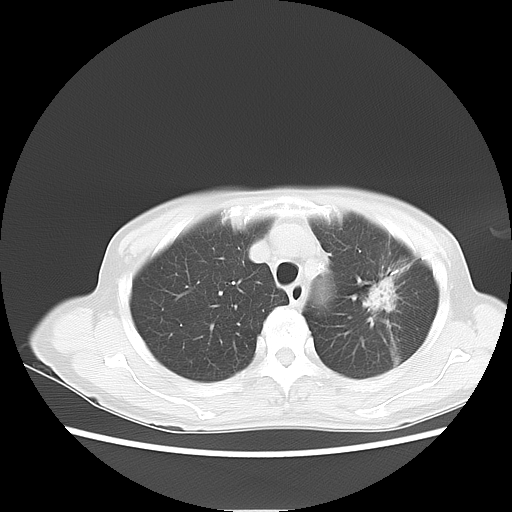
Chest CT, one axial slice. Position 8 of 13 along the scan axis. Reconstruction kernel LUNG. Lung window (W 1500 / L -600 HU). 5 mm slice thickness. 512 × 512 image matrix, field of view 350 × 350 mm. Female patient, age 71 years. Case-level facts recorded for this patient, not image findings: clinical TNM (as recorded): T2 N0 M0.
Outlined on this slice (rectangle marked by the reading radiologist):
- lung tumour (recorded histology: adenocarcinoma): bounding box [x1, y1, x2, y2] px = [360, 270, 401, 319]